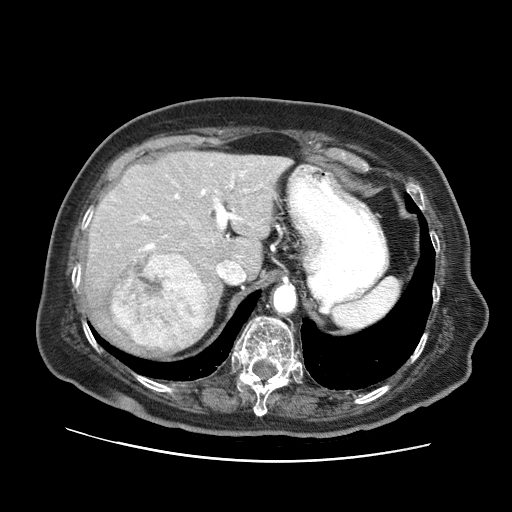
Contrast-enhanced abdominal CT (liver protocol), one axial slice; slice 48 of 73 in the series (ordered by position); soft-tissue window (W 400 / L 40 HU); 2.5 mm slice thickness; 512 × 512 image matrix. From the clinical record (not read from this slice): diagnosis: hepatocellular carcinoma (patient treated with transarterial chemoembolisation; whether this scan precedes or follows treatment is not stated here); TNM stage (as recorded): Stage-I; Child-Pugh class: A; tumour differentiation: well differentiated; tumour nodularity: uninodular.
Structures marked on this image (semi-automatically segmented with operator editing):
- liver parenchyma outside the tumour (the mass and vessels are separate outlines, so this box may not span the whole liver): bounding box [x1, y1, x2, y2] px = [83, 150, 292, 360]
- mass: [110, 254, 207, 350]
- liver vessels: [140, 164, 247, 251]